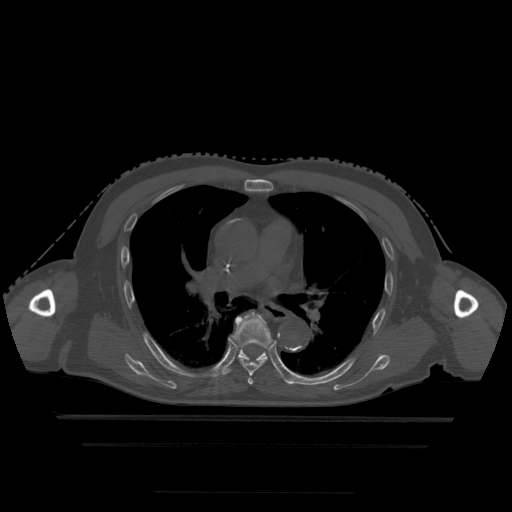
CT including the spine, one axial slice. Position 311 of 522 along the scan axis. Bone window (W 1800 / L 400 HU). 1.25 mm slice thickness. 512 × 512 image matrix. Patient age 68 years. Case-level facts recorded for this patient, not image findings: primary cancer: urothelial.
Outlined on this slice (semi-automatically segmented with operator editing):
- T5 vertebra: bounding box (x1, y1, x2, y2) in pixels: (248, 375, 254, 385)
- T6 vertebra: (234, 312, 272, 376)
- T7 vertebra: (223, 343, 286, 381)